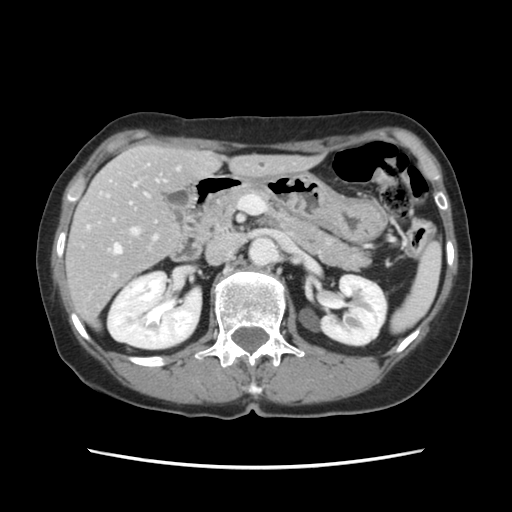
Contrast-enhanced abdominal CT, one axial slice; position 62 of 120 along the scan axis; 120 kVp; intravenous contrast given; soft-tissue window (W 400 / L 40 HU); 512 × 512 image matrix. Female patient, age 70 years. From the clinical record (not read from this slice): diagnosis: colorectal cancer liver metastases, imaged before liver resection; multiple liver metastases: no; largest metastasis: 2.5 cm; disease in both lobes: no.
Structures marked on this image (expert manual segmentation):
- hepatic veins: box from (x=87, y=180) to (x=158, y=254) px
- liver: (x=68, y=146)–(x=311, y=323)
- planned liver remnant (the part of the liver to remain after resection): (x=73, y=146)–(x=311, y=283)
- portal vein (with intrahepatic branches): (x=100, y=168)–(x=179, y=239)